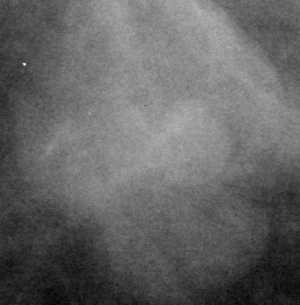
Cropped region of a digitized screen-film mammogram centred on a radiologist-marked abnormality, left breast, CC view, BI-RADS breast density category 2 (scale 1–4).
Finding: mass, shape lobulated, margins circumscribed; BI-RADS assessment category 4; subtlety rating 3 on a 1 (subtle) to 5 (obvious) scale; pathology (as recorded): benign.